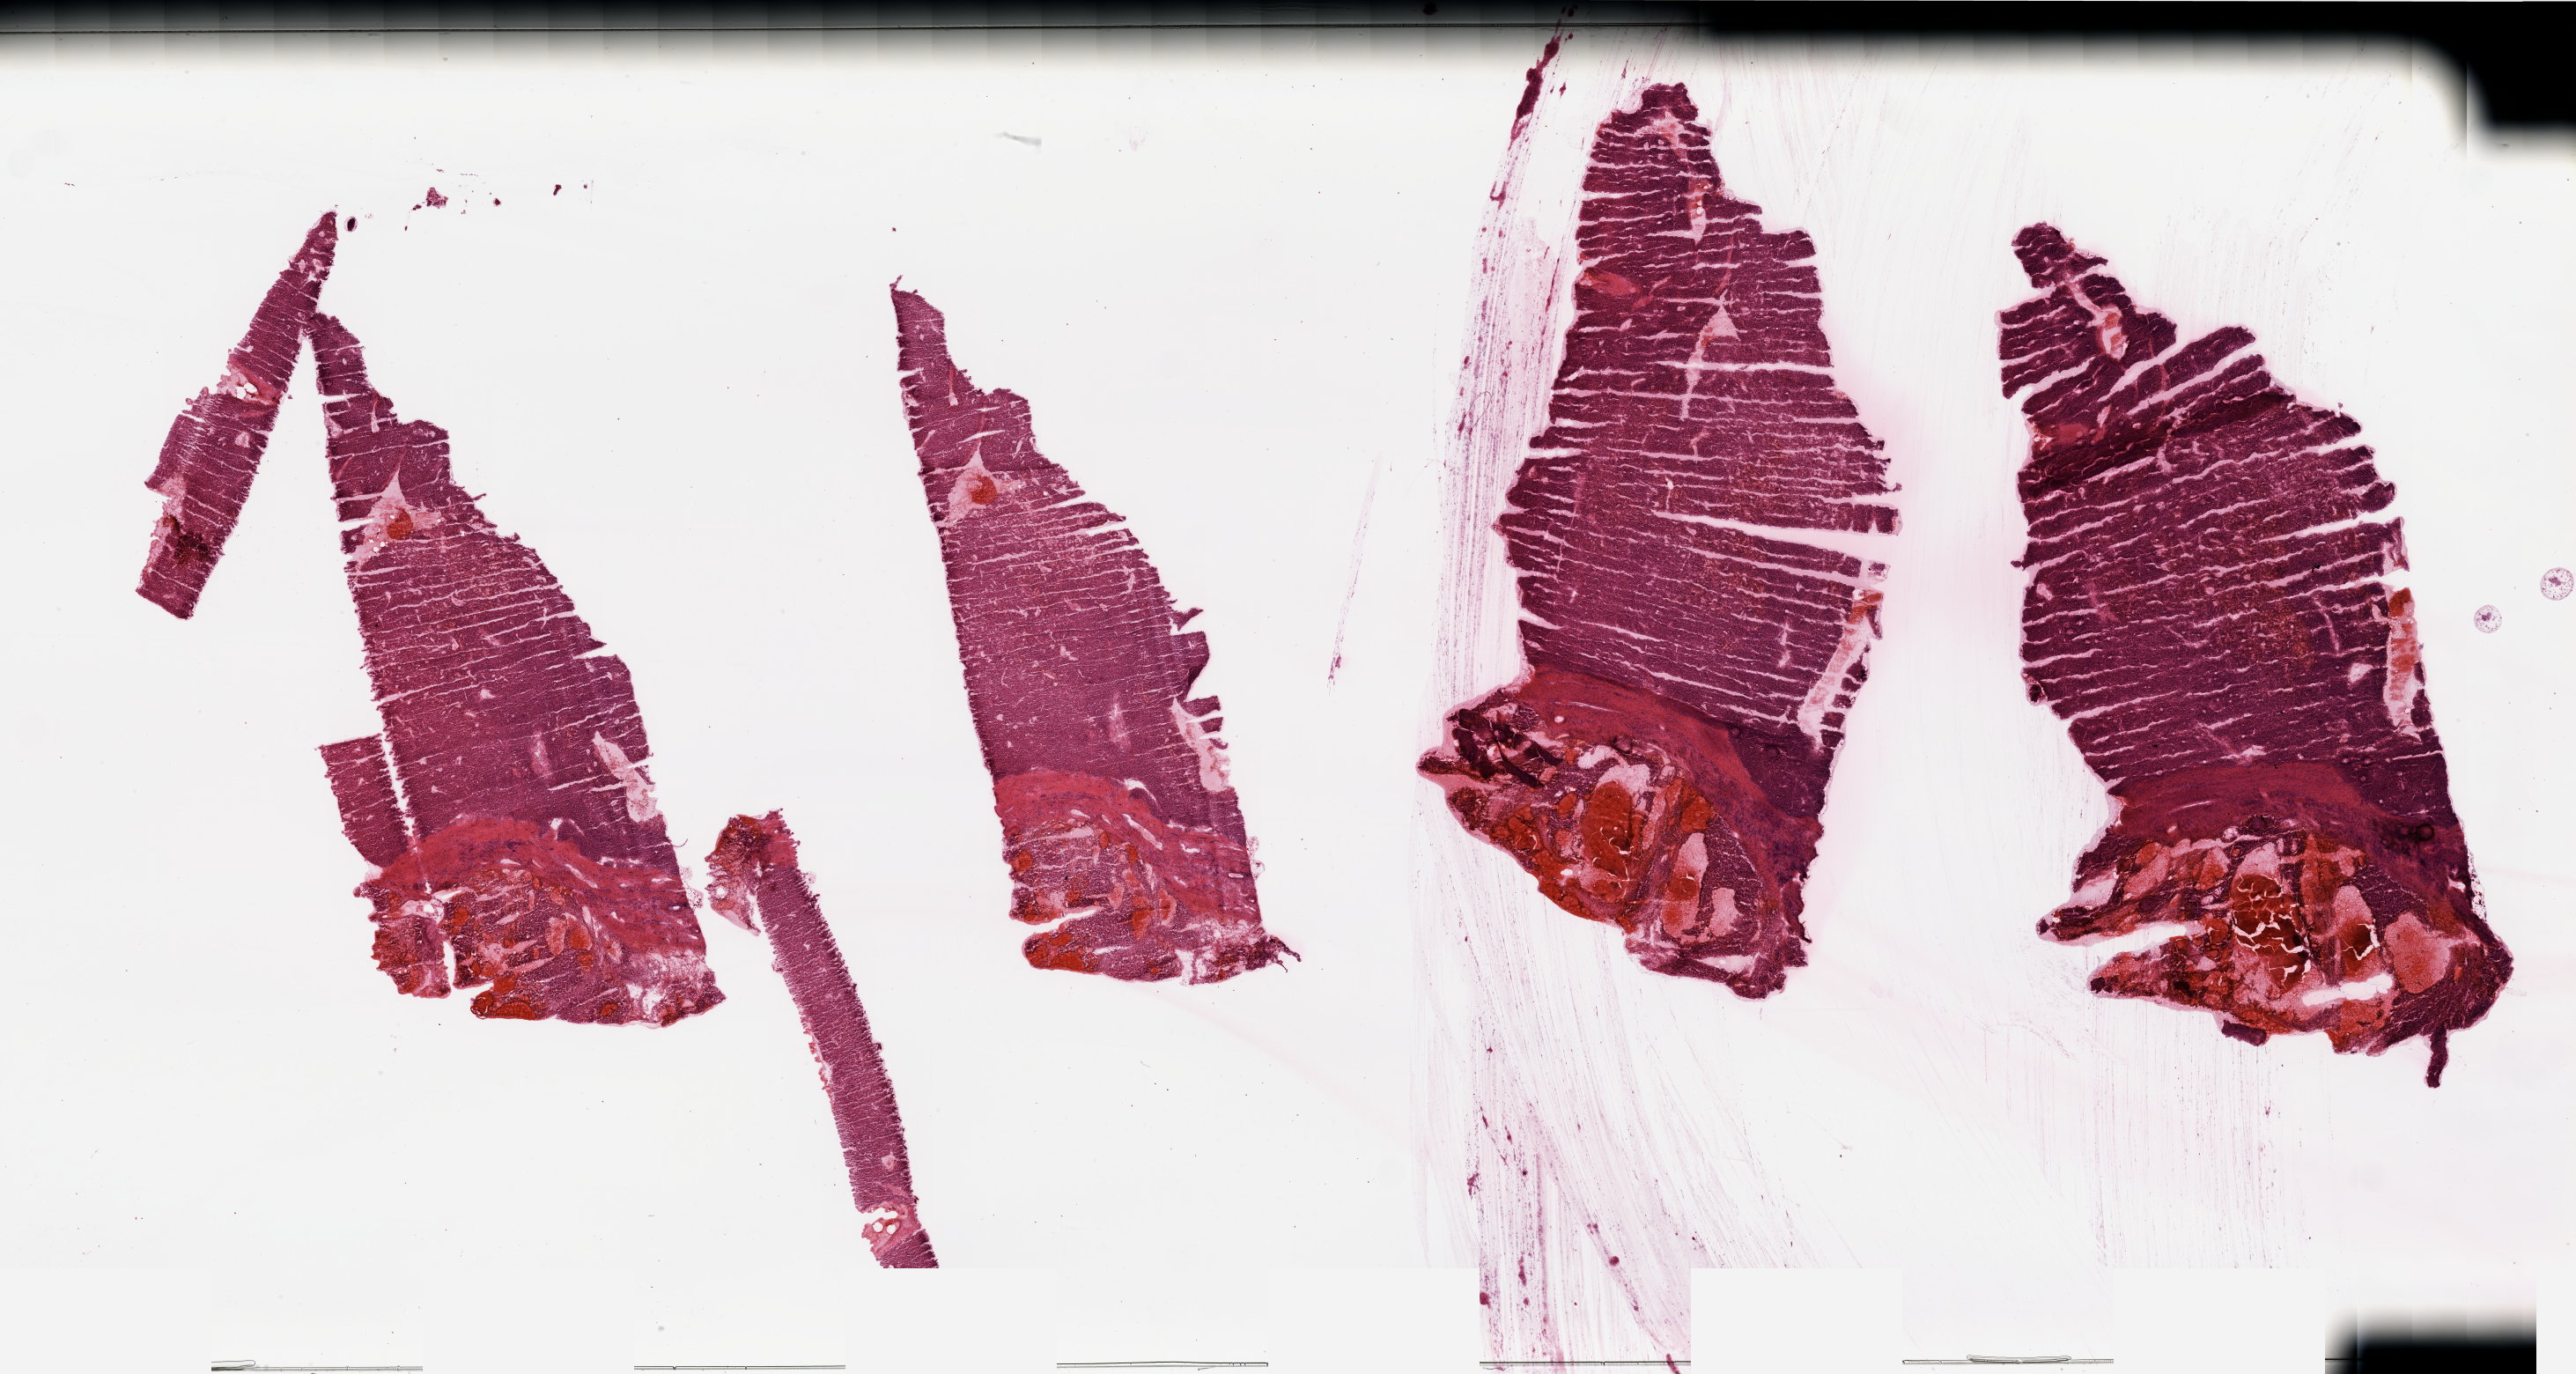
H&E-stained whole-slide image, low-resolution overview of the scanned area, about 46.3 x 24.7 mm (from a 20x scan), tumour tissue sample, sampled site: kidney. 66-year-old male patient. Histologic grade: G2 (moderately differentiated). Composition of this section per pathologist review: tumour nuclei 85%, necrosis 10%.
Primary tumour site (as recorded): upper pole. AJCC pathologic stage: I. Diagnosis: Renal cell carcinoma, NOS.